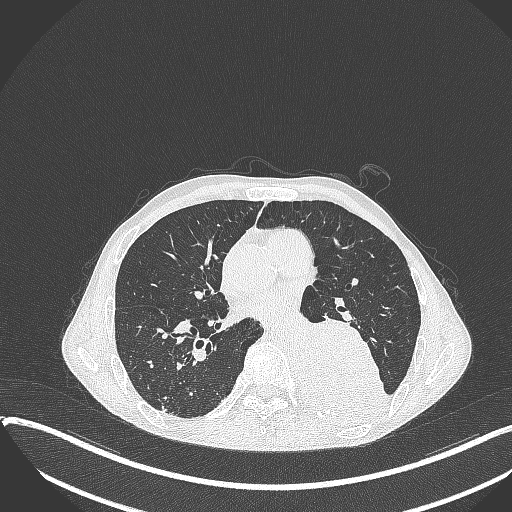
Chest CT, one axial slice; position 179 of 401 along the scan axis; reconstruction kernel B70f; 120 kVp; lung window (W 1500 / L -600 HU); 1 mm slice thickness; 512 × 512 image matrix, field of view 400 × 400 mm. Male patient, age 57 years. Case-level facts recorded for this patient, not image findings: clinical TNM (as recorded): T4 N0 M0.
Structures marked on this image (rectangle marked by the reading radiologist):
- lung tumour (recorded histology: squamous cell carcinoma): bounding box (x1, y1, x2, y2) in pixels: (304, 312, 387, 425)